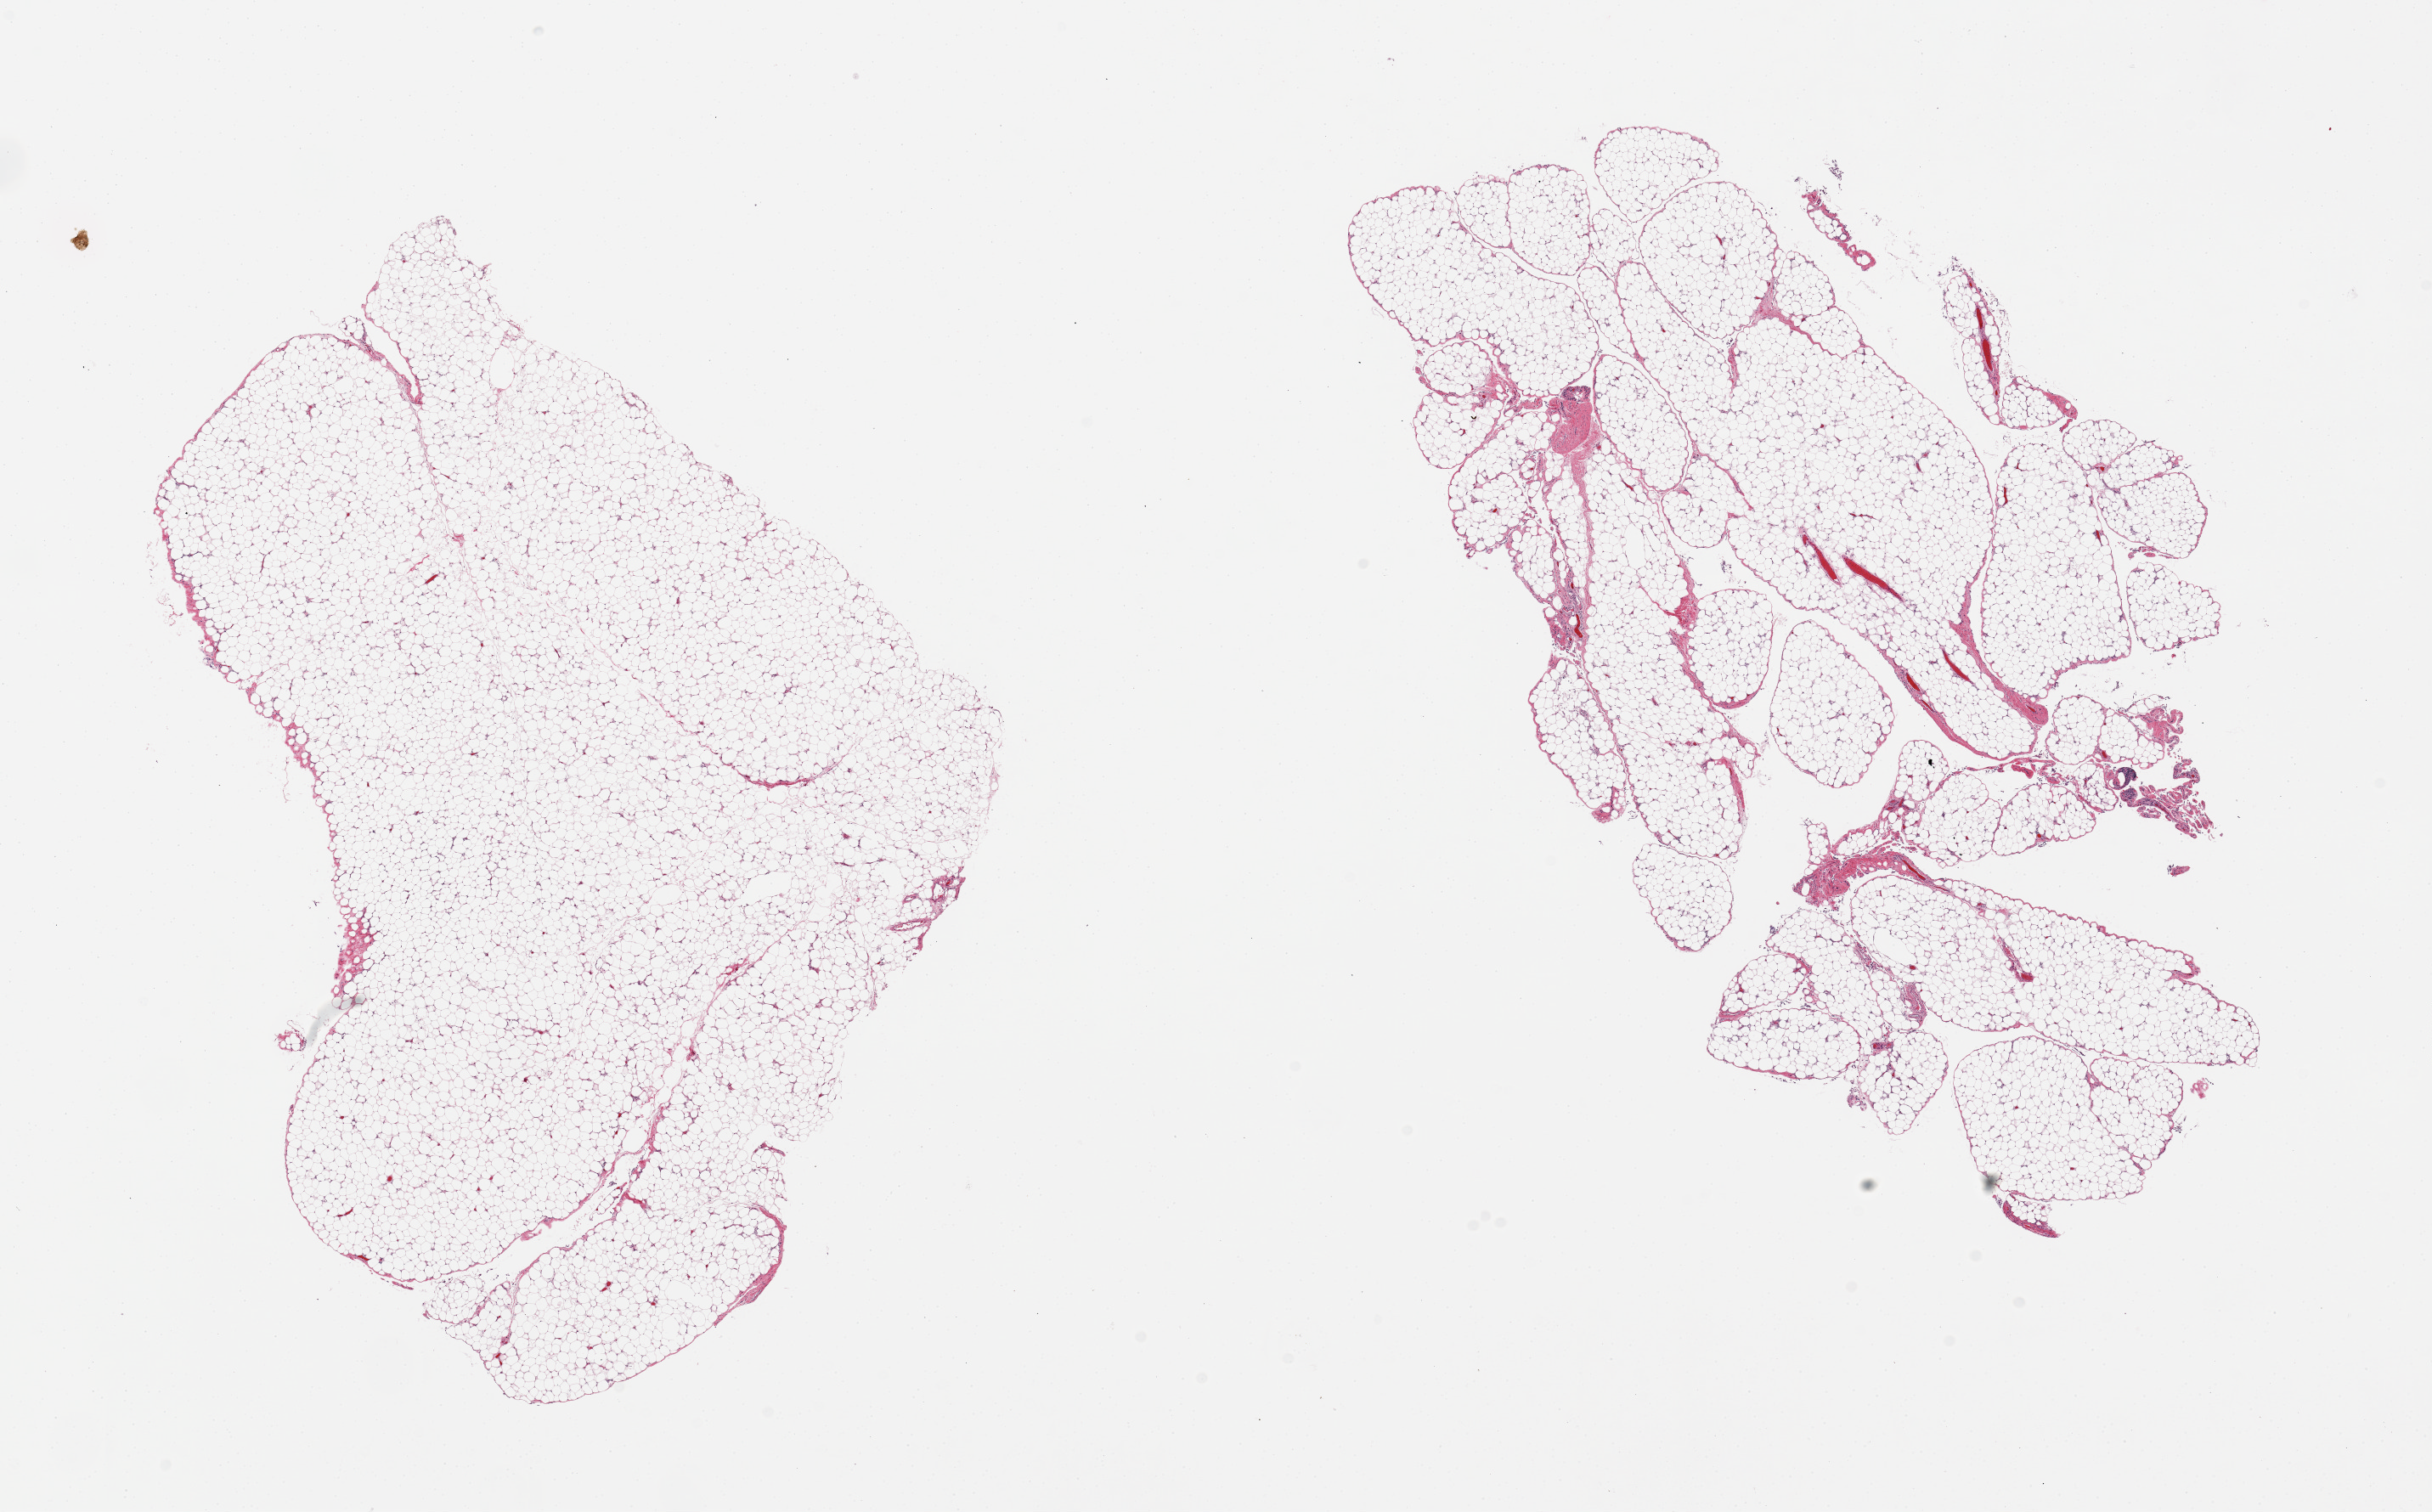
Hematoxylin and eosin (H&E) whole-slide image — whole scanned area (about 22.6 x 14.1 mm, from a 20x scan) shown as a low-resolution overview; PAXgene-fixed, paraffin-embedded tissue; target tissue: omentum; donor tissue sample. Donor sex: male.
Pathologist's review note for this sample: 2 pieces.